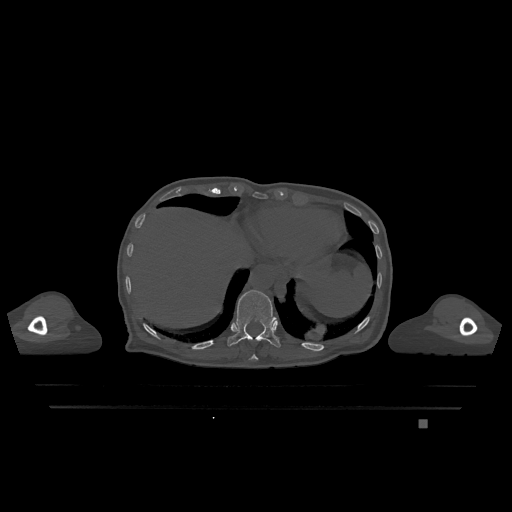
CT including the spine, one axial slice; position 598 of 1317 along the scan axis; bone window (W 1800 / L 400 HU); 512 × 512 image matrix, field of view 500 × 500 mm. Female patient, age 74 years. Case-level facts recorded for this patient, not image findings: primary cancer: lung.
Outlined on this slice (semi-automatic segmentation, software-assisted and operator-edited):
- T10 vertebra: bounding box <249,354,258,361> (left, top, right, bottom; pixels)
- T11 vertebra: <228,290,281,348>